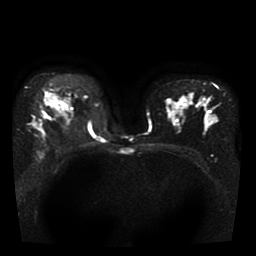
Breast MRI, one axial slice. Slice 27 of 41 in the series (ordered by position). Diffusion-weighted series; image 2 of 4 stored at this slice position (different b-values; order by instance number). 1.5 T. 5 mm slice thickness. 256 × 256 image matrix, field of view 330 × 330 mm. Female patient.
Structures marked on this image (outlined manually by an expert reader):
- tumour on diffusion-weighted imaging: box from (x=33, y=123) to (x=45, y=136) px